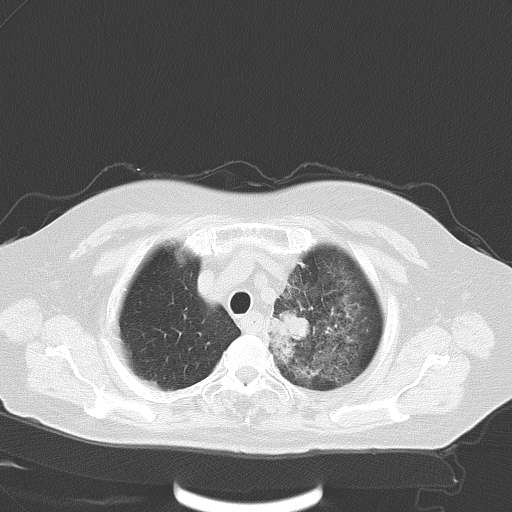
Chest CT, one axial slice; position 47 of 56 along the scan axis; reconstruction kernel B70f; 120 kVp; lung window (W 1500 / L -600 HU); 512 × 512 image matrix. Female patient, age 65 years. From the clinical record (not read from this slice): clinical TNM (as recorded): T2b N1 M0.
Outlined on this slice (rectangle marked by the reading radiologist):
- lung tumour (recorded histology: adenocarcinoma): bounding box (x1, y1, x2, y2) in pixels: (270, 306, 317, 343)